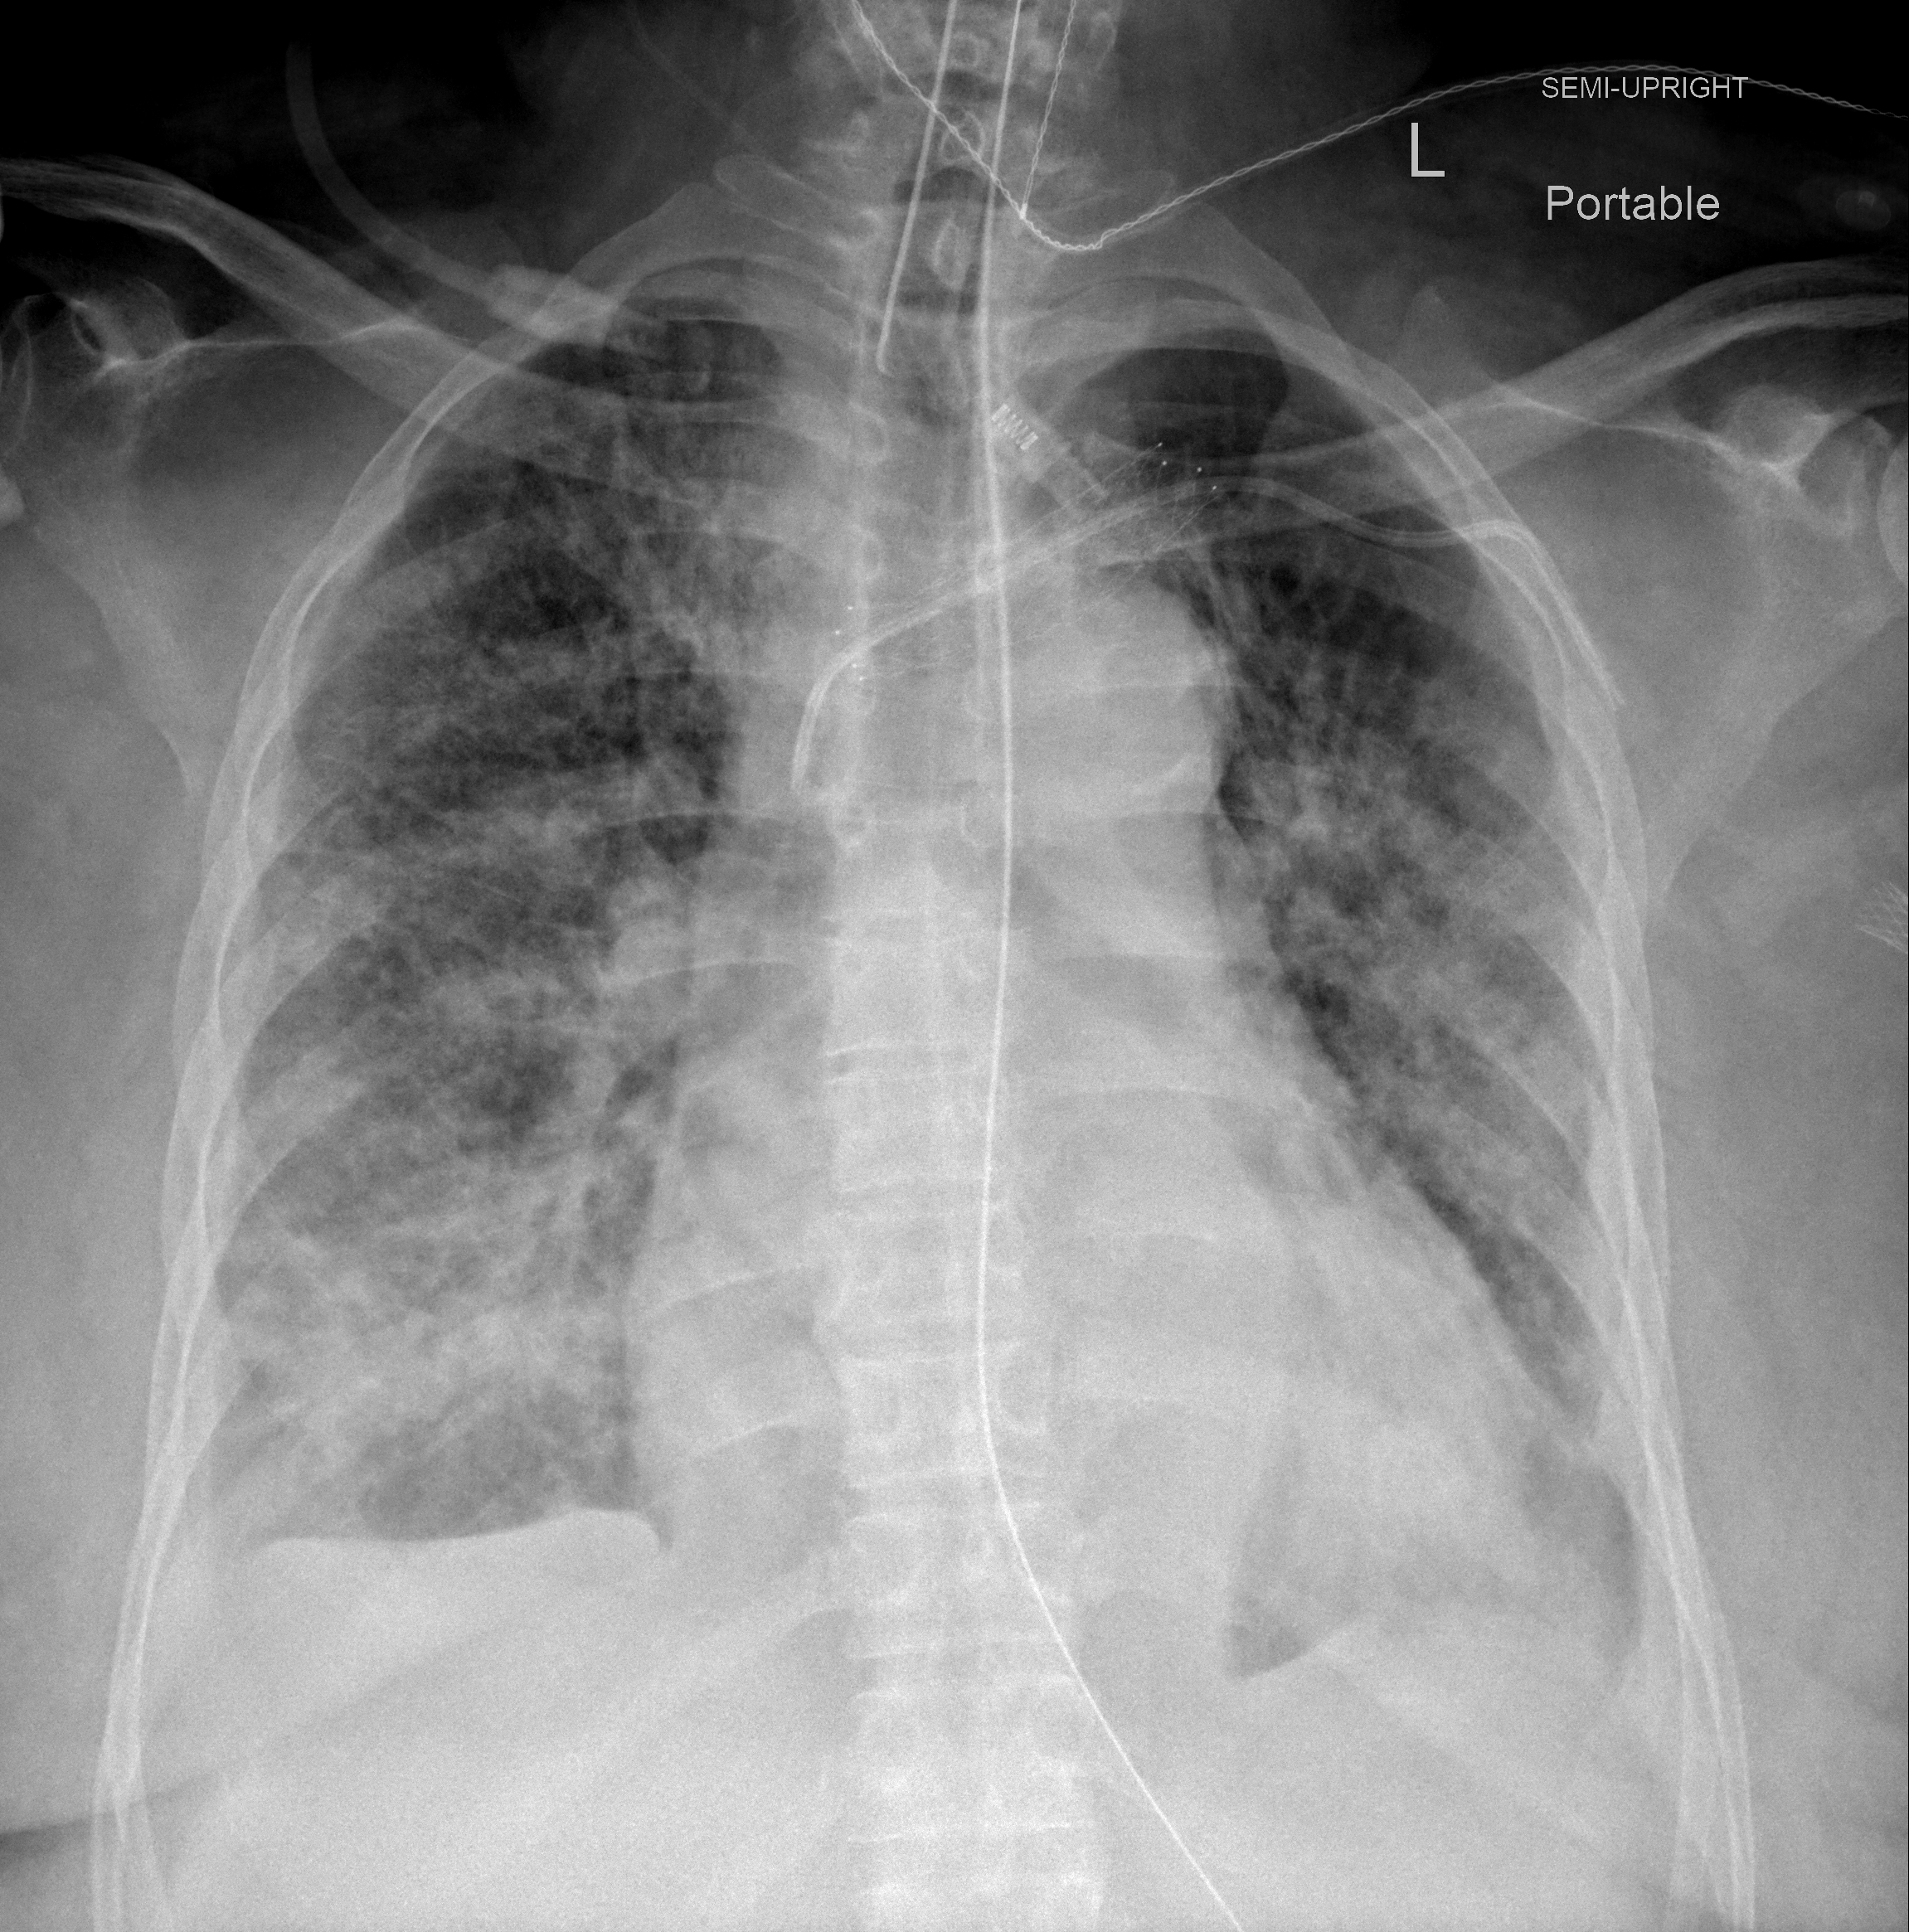
Portable chest radiograph, AP projection. Female patient, age 64 years; COVID-19 (test-positive).
Key findings recorded by the radiologist: Interval development of diffuse bilateral airspace disease with only partial sparing of the left lung apex.